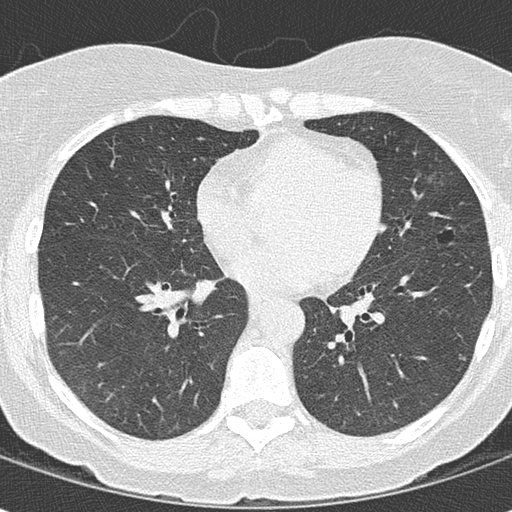
Chest CT (low-dose screening protocol), one axial image; second screening round (one year after baseline); lung window (W 1500 / L -600 HU); lung (sharp) reconstruction kernel (B50f); 512 × 512 image matrix, field of view 274 × 274 mm. Female, age 63 years at enrolment. Current smoker at enrolment.
Expert reader's lesion annotation, bounding box (x1, y1, x2, y2) in pixels: (418, 211, 475, 256). The screening reader recorded 4 non-calcified nodules or masses ≥4 mm on this exam; which of them this box marks is not recorded. Official screen result: positive, other. Later outcome: lung cancer diagnosed 504 days after this screen (after the third annual screen) — bronchiolo-alveolar adenocarcinoma, NOS, lingula, stage IA (AJCC 6th edition), 14 mm at pathology.